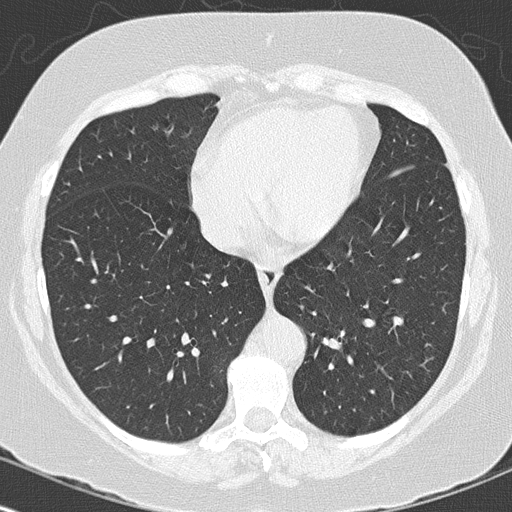
Low-dose screening chest CT, one axial slice; slice 52 of 144 in the series (ordered by position); reconstruction kernel B50f; lung window (W 1500 / L -600 HU); 512 × 512 image matrix, field of view 316 × 316 mm.
Annotated regions visible in this slice (outlined manually by an expert reader):
- lesion 1 (tumor, lower lobe of left lung): bounding box <361,302,369,309> (left, top, right, bottom; pixels)